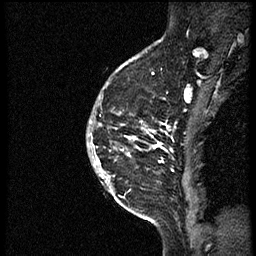
Breast MRI (dynamic contrast-enhanced), one sagittal slice. Position 43 of 56 along the scan axis. Dynamic contrast-enhanced study with each time point stored as its own series, time point 2 of 3 at this slice position (early post-contrast, ordered by acquisition time). 1.5 T. TE 4.2 ms, TR 21.3 ms. 256 × 256 image matrix. Patient: female, 41 years. From the clinical record (not read from this slice): setting: breast cancer imaged before/during neoadjuvant chemotherapy; receptor status: HER2-positive.
Outlined on this slice (semi-automatically segmented with operator editing):
- analysis volume of interest (the breast-tissue region the enhancement analysis was run in; not a lesion): bounding box [x1, y1, x2, y2] px = [93, 73, 175, 205]
- tumour enhancement mask (voxels above the 100 % enhancement threshold inside the analysis volume of interest): [100, 124, 169, 180]